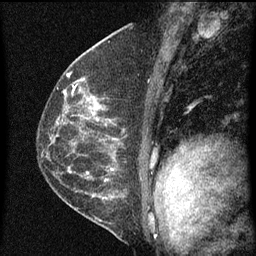
Breast MRI (dynamic contrast-enhanced), one sagittal slice; slice 38 of 60 in the series (ordered by position); dynamic contrast-enhanced series, image 2 of 4 at this slice position (ordered by acquisition); 1.5 T; TE 4.2 ms, TR 8 ms; 2 mm slice thickness; 256 × 256 image matrix, field of view 180 × 180 mm. Female patient, age 48 years.
Annotated regions visible in this slice (semi-automatically segmented with operator editing):
- analysis volume of interest (the breast-tissue region the enhancement analysis was run in; not a lesion): bounding box [x1, y1, x2, y2] px = [73, 82, 115, 139]
- tumour enhancement mask (voxels above the 70 % enhancement threshold inside the analysis volume of interest): [73, 84, 100, 117]